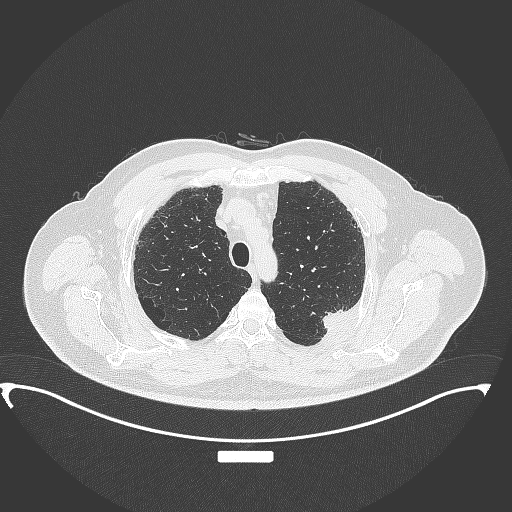
Chest CT, one axial slice; slice 288 of 350 in the series (ordered by position); 120 kVp; lung window (W 1500 / L -600 HU); 1 mm slice thickness; 512 × 512 image matrix, field of view 459 × 459 mm. Patient: male, 64 years. From the clinical record (not read from this slice): clinical TNM (as recorded): T1c N1 M1.
Outlined on this slice (bounding box drawn by a radiologist):
- lung tumour (recorded histology: adenocarcinoma): bounding box [x1, y1, x2, y2] px = [315, 304, 350, 333]